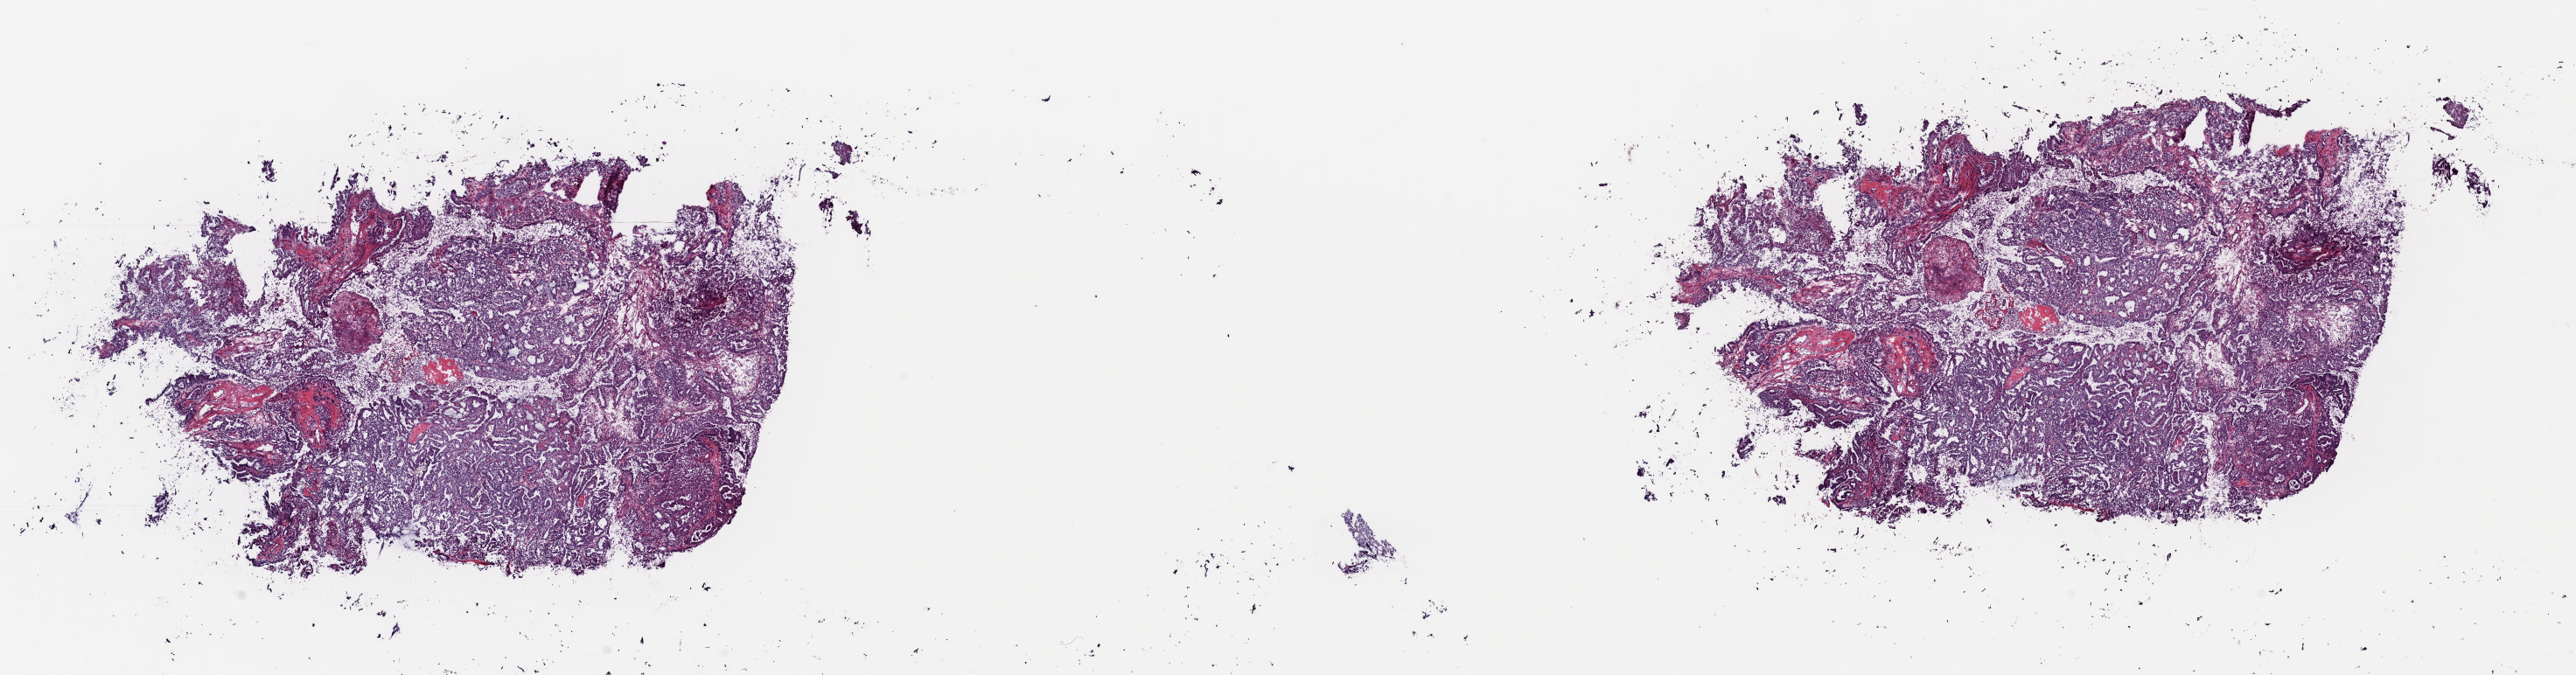
Digitized H&E tissue section (whole slide) — low-resolution overview of the scanned area, about 23.3 x 6.1 mm (slide scanned at 40x); frozen section from the top of the tissue portion; uterus, primary tumour sample. Patient: female, age at initial diagnosis 77 years. Histologic grade: G3 (poorly differentiated). Pathologist review of this section (percent, as recorded): tumour cells 90%, tumour nuclei 85%, normal cells 0%, stromal cells 5%, necrosis 5%. Inflammatory infiltration, as recorded: lymphocyte infiltration 2%, monocyte infiltration 0%, neutrophil infiltration 0%.
* FIGO stage: IIIC1
* lymph nodes positive (case pathology): 1 of 34 examined
* diagnosis: Endometrioid adenocarcinoma, NOS (endometrium)